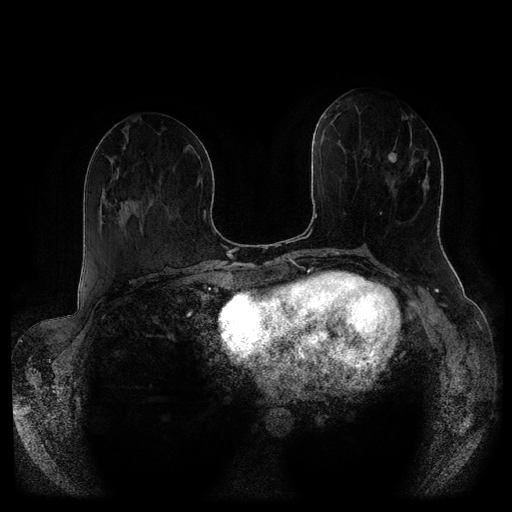
Breast MRI (dynamic contrast-enhanced, multi-phase), one axial slice. Position 40 of 116 along the scan axis. Dynamic contrast-enhanced series, time point 2 of 5 at this slice position (early post-contrast). 1.5 T. TE 2.6 ms, TR 5.3 ms. 512 × 512 image matrix. Patient: female, 51 years.
Structures marked on this image (semi-automatically segmented with operator editing):
- breast lesion (labelled 'tumour' in the annotation; benign lesions carry a separate 'benign' label): bounding box [x1, y1, x2, y2] px = [388, 147, 398, 163]